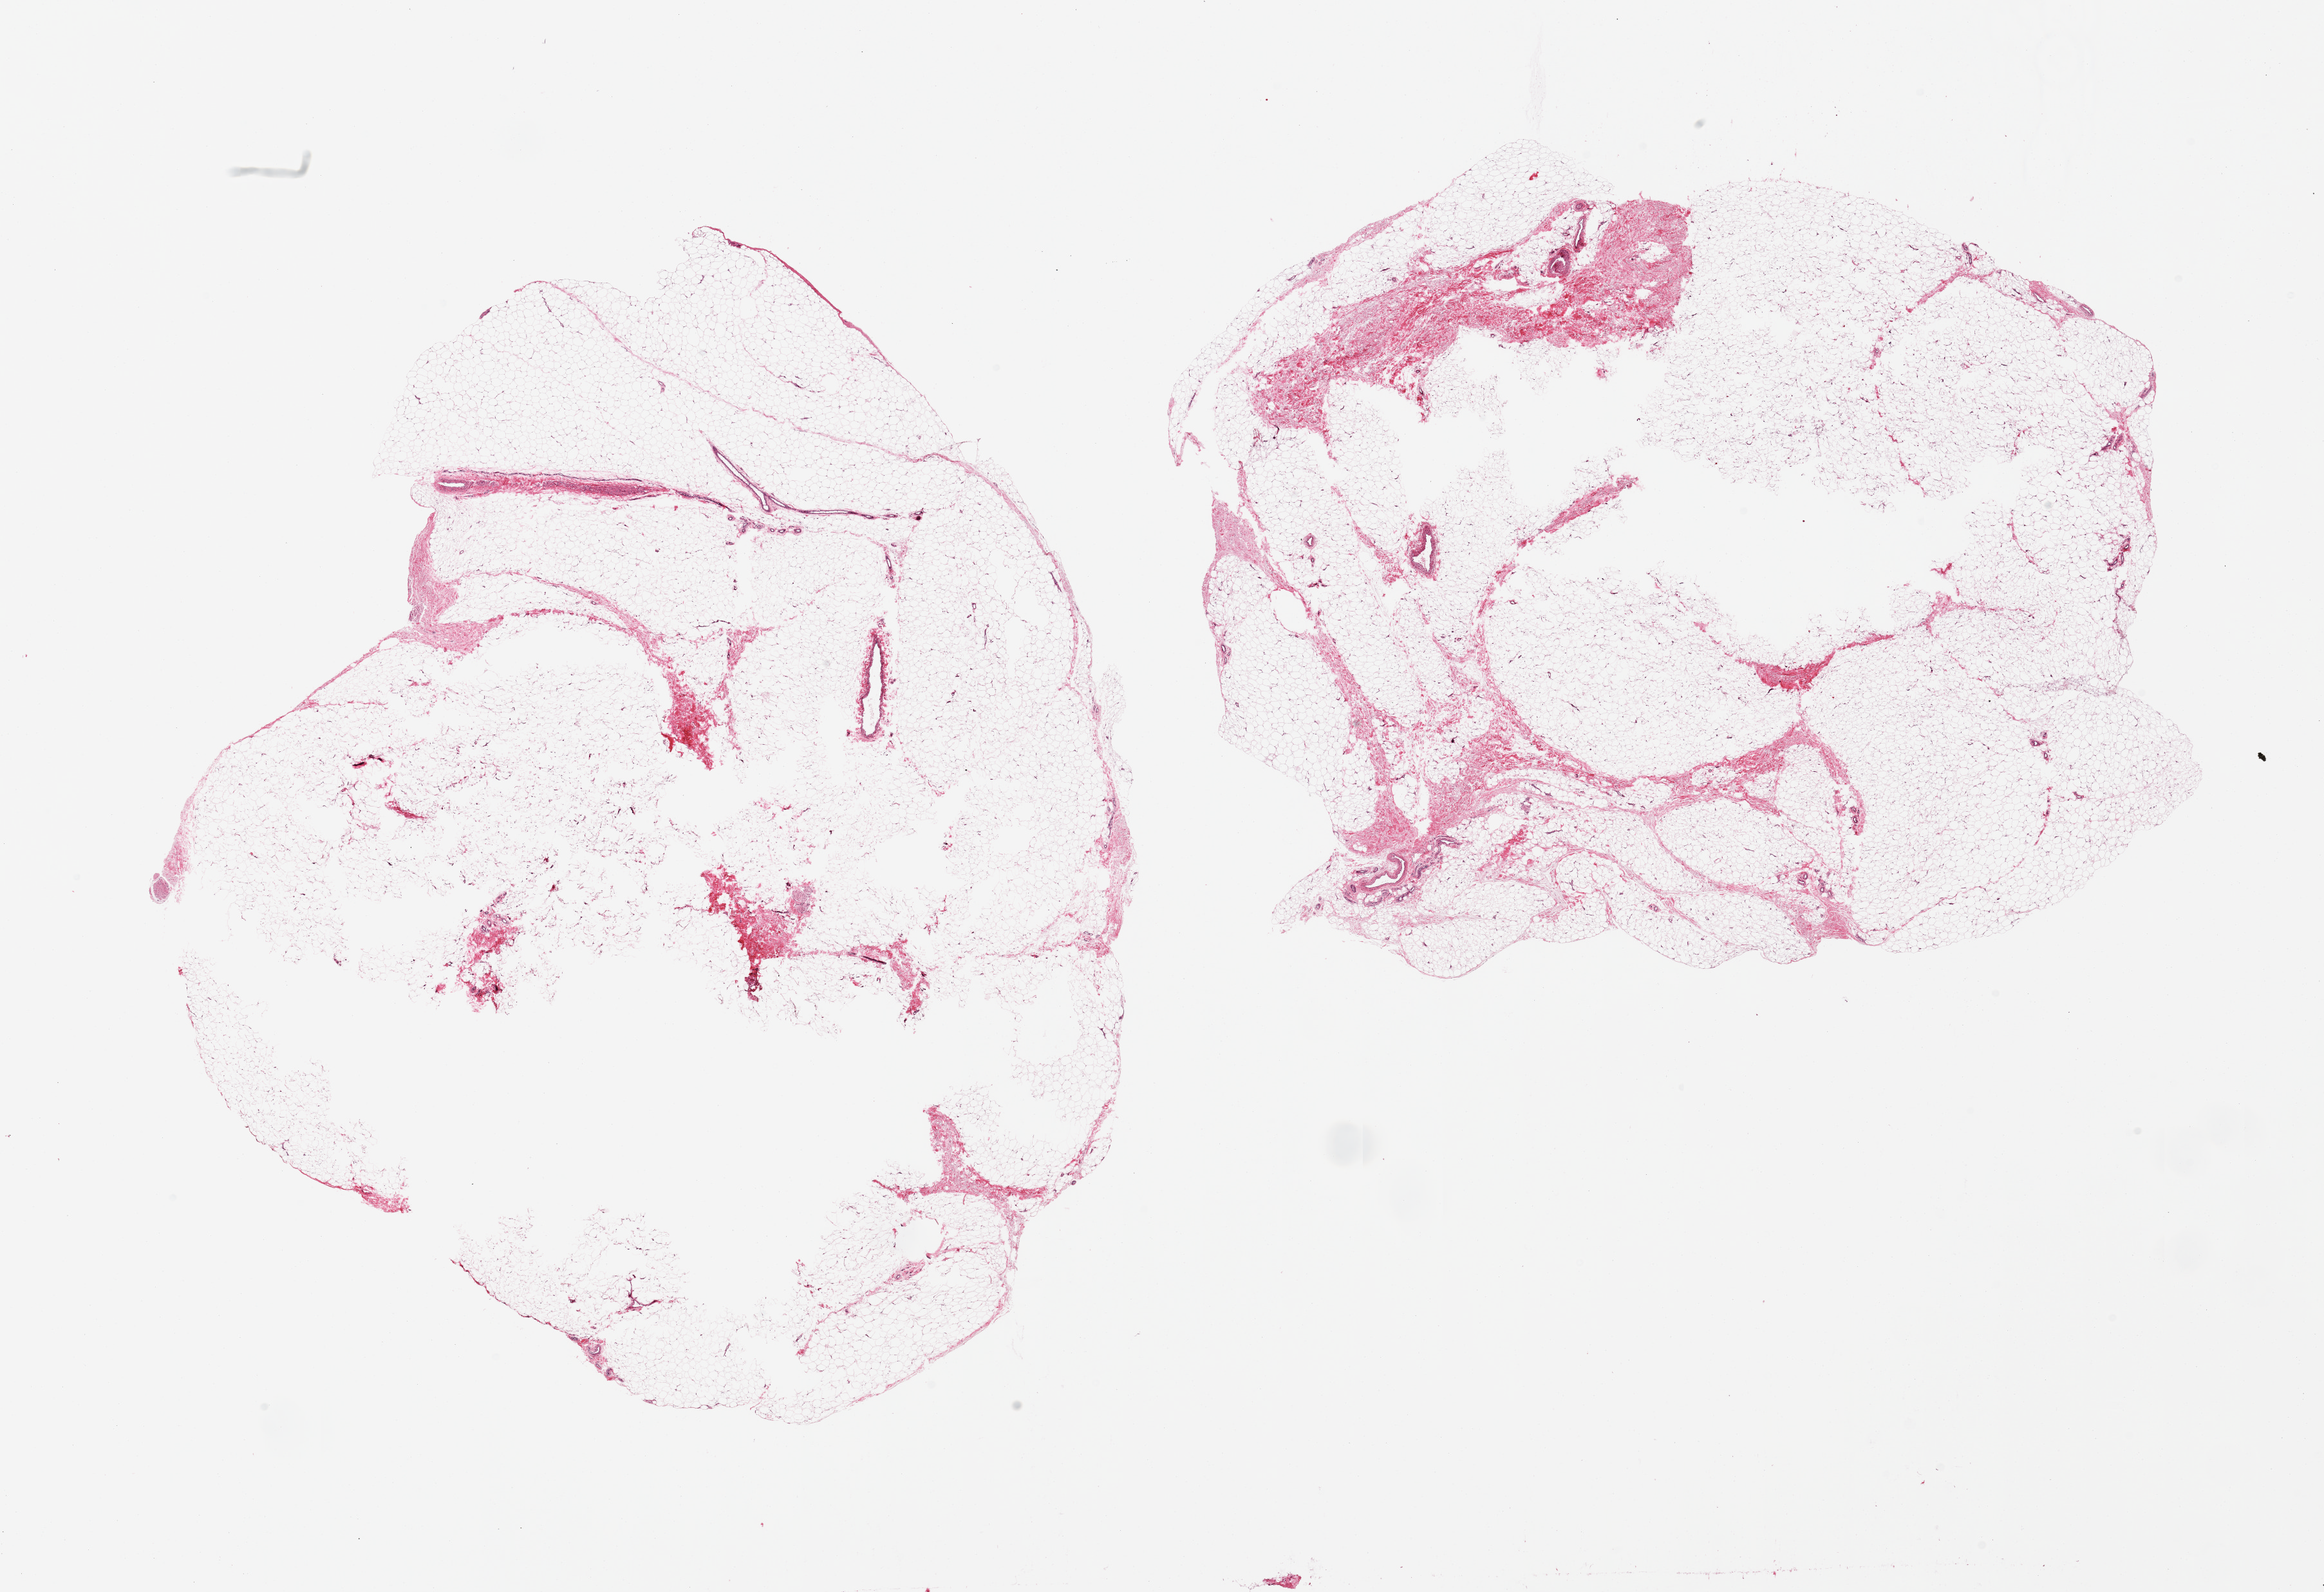
Whole-slide image, hematoxylin and eosin (H&E) stain — low-resolution overview of the scanned area, about 28.5 x 19.6 mm, PAXgene-fixed paraffin-embedded (PFPE) section, sampled site (target tissue): adipose tissue, donor tissue sample.
- pathologist's review note for this sample: 2 pieces, central defects in both (?poor fixation)